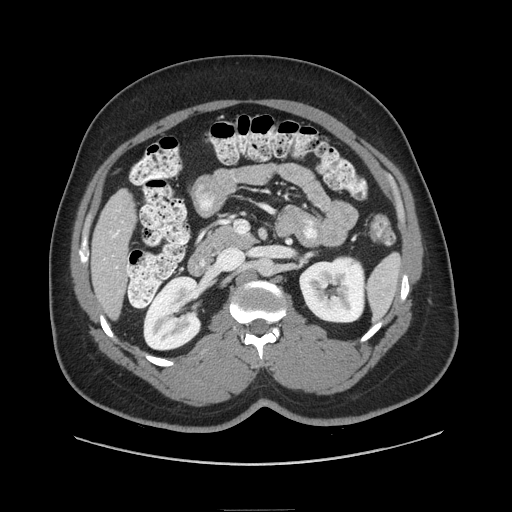
Contrast-enhanced abdominal CT (liver protocol), one axial slice. Slice 25 of 87 in the series (ordered by position). Soft-tissue window (W 400 / L 40 HU). 512 × 512 image matrix. From the clinical record (not read from this slice): diagnosis: hepatocellular carcinoma (patient treated with transarterial chemoembolisation; whether this scan precedes or follows treatment is not stated here); TNM stage (as recorded): Stage-II; Child-Pugh class: A; tumour nodularity: uninodular.
Structures marked on this image (semi-automatically segmented with operator editing):
- liver parenchyma outside the tumour (the mass and vessels are separate outlines, so this box may not span the whole liver): box from (x=90, y=188) to (x=136, y=318) px
- liver vessels: (x=112, y=210)–(x=120, y=268)